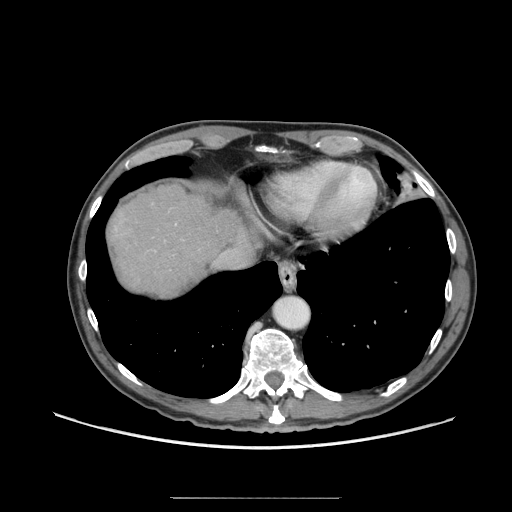
Contrast-enhanced abdominal CT (liver protocol), one axial slice; slice 60 of 71 in the series (ordered by position); reconstruction kernel STANDARD; 140 kVp; soft-tissue window (W 400 / L 40 HU); 2.5 mm slice thickness; 512 × 512 image matrix, field of view 400 × 400 mm. Case-level facts recorded for this patient, not image findings: diagnosis: hepatocellular carcinoma (patient treated with transarterial chemoembolisation; whether this scan precedes or follows treatment is not stated here); TNM stage (as recorded): Stage-I; Child-Pugh class: A; tumour nodularity: uninodular; tumour size: 3.5 cm.
Annotated regions visible in this slice (semi-automatic segmentation, software-assisted and operator-edited):
- abdominal aorta: bounding box [x1, y1, x2, y2] px = [274, 297, 309, 329]
- liver parenchyma outside the tumour (the mass and vessels are separate outlines, so this box may not span the whole liver): [108, 186, 252, 296]
- mass: [108, 214, 130, 240]